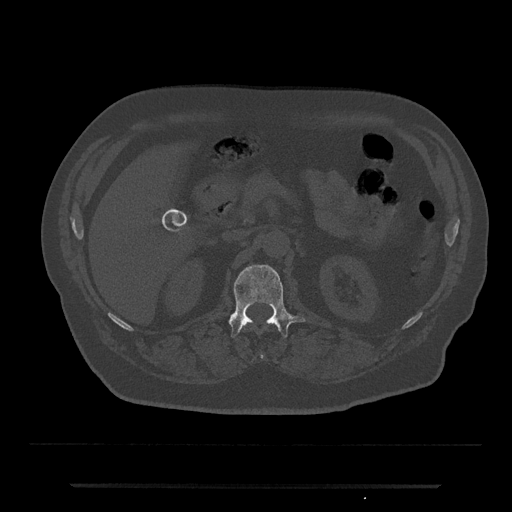
CT including the spine, one axial slice; slice 547 of 797 in the series (ordered by position); reconstruction kernel Br40s/3; bone window (W 1800 / L 400 HU); 0.5 mm slice thickness; 512 × 512 image matrix. Patient: male, 80 years. Case-level facts recorded for this patient, not image findings: primary cancer: prostate; vertebrae with lytic lesions (as recorded): L1, T11.
Structures marked on this image (semi-automatic segmentation, software-assisted and operator-edited):
- L1 vertebra: bounding box (x1, y1, x2, y2) in pixels: (228, 265, 305, 337)